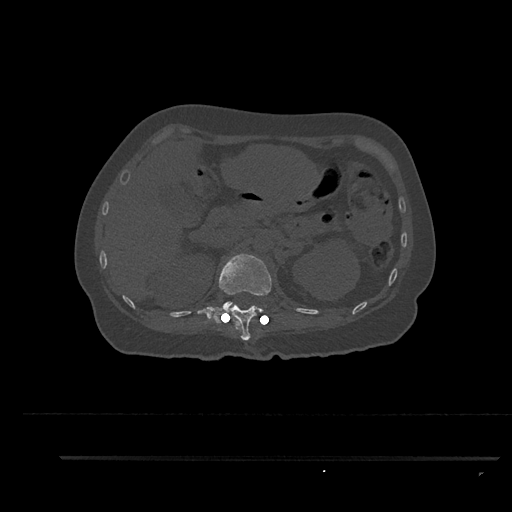
CT including the spine, one axial slice. Slice 245 of 797 in the series (ordered by position). Reconstruction kernel Br40s/3. Bone window (W 1800 / L 400 HU). 0.5 mm slice thickness. 512 × 512 image matrix, field of view 408 × 408 mm. Female patient, age 44 years. From the clinical record (not read from this slice): primary cancer: renal.
Annotated regions visible in this slice (semi-automatic segmentation, software-assisted and operator-edited):
- L1 vertebra: bounding box [x1, y1, x2, y2] px = [223, 301, 233, 309]
- T12 vertebra: [197, 253, 272, 340]